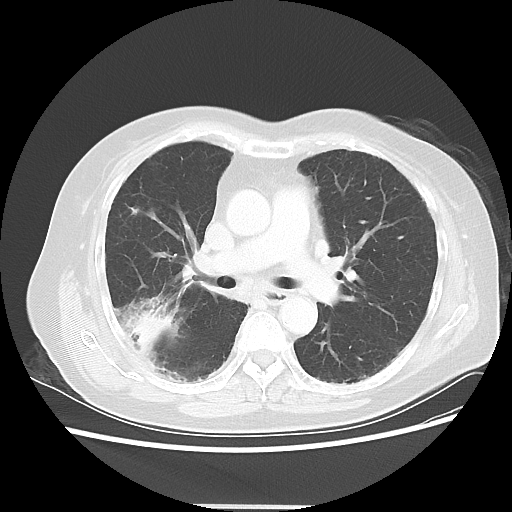
Chest CT, one axial slice. Position 28 of 50 along the scan axis. 120 kVp. Lung window (W 1500 / L -600 HU). 5 mm slice thickness. 512 × 512 image matrix, field of view 360 × 360 mm. Patient: female, 72 years. From the clinical record (not read from this slice): clinical TNM (as recorded): T2 N1 M0.
Structures marked on this image (rectangle marked by the reading radiologist):
- lung tumour (recorded histology: adenocarcinoma): bounding box (x1, y1, x2, y2) in pixels: (127, 311, 176, 352)